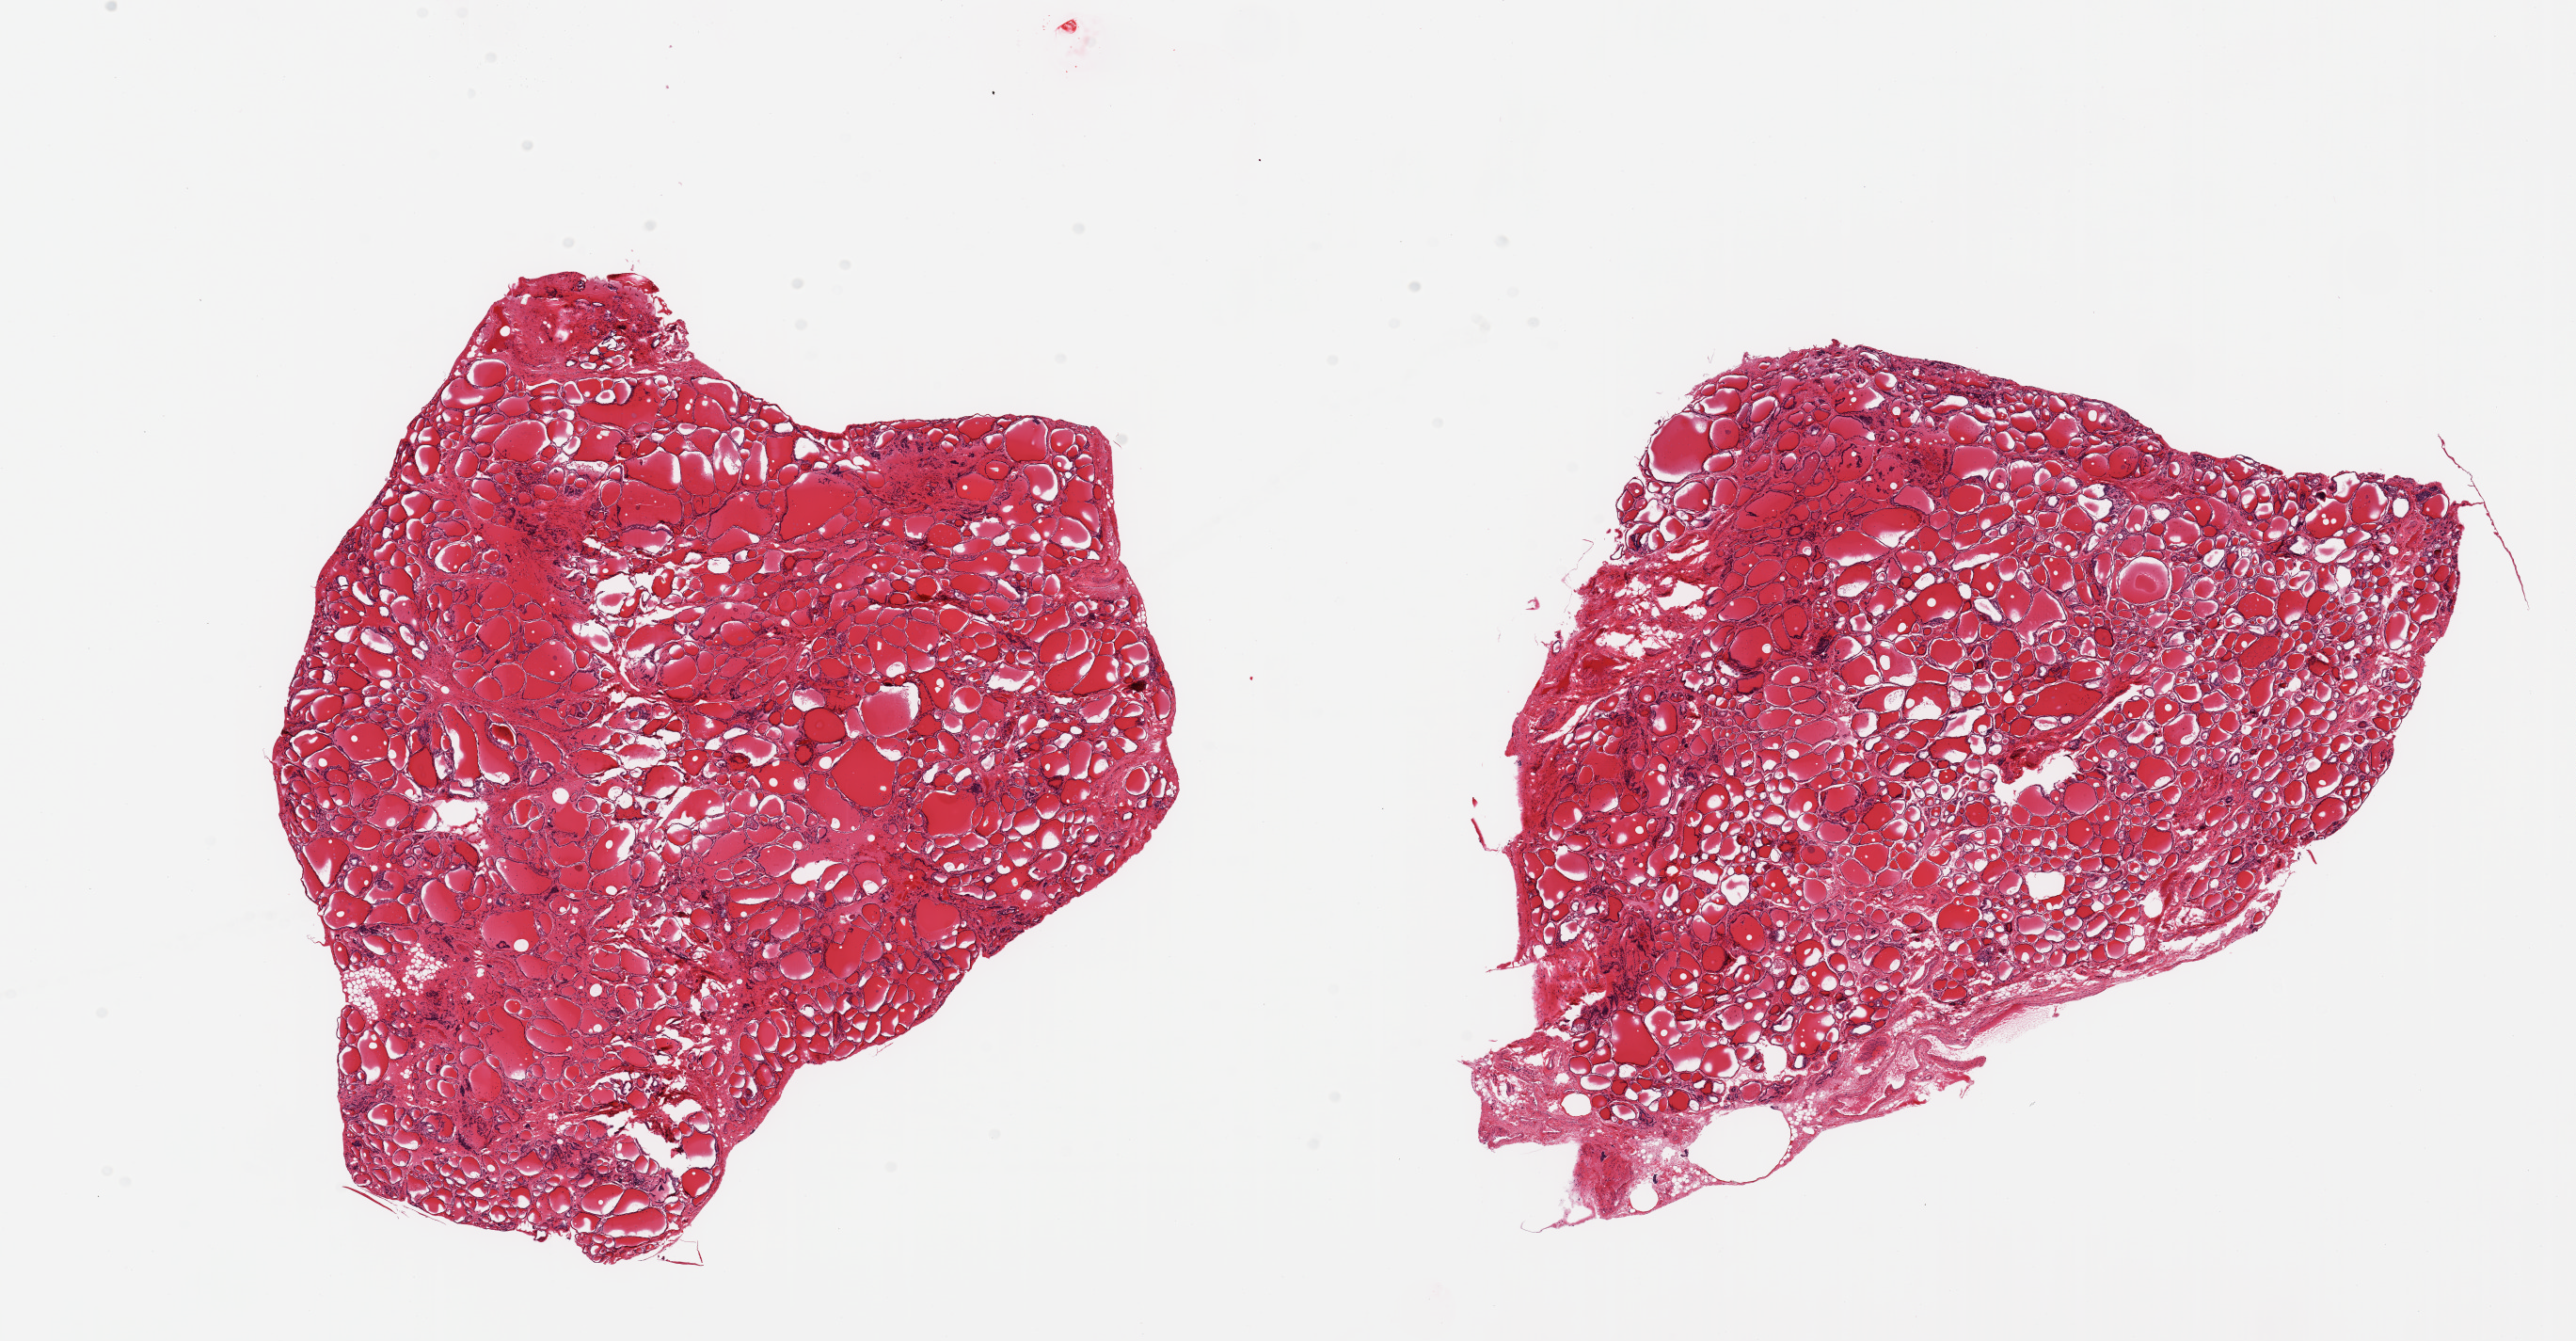
H&E whole-slide image — a low-resolution overview of the entire scanned area, about 21.7 x 11.3 mm (slide scanned at 20x); PAXgene-fixed paraffin-embedded (PFPE) section; section of thyroid (target tissue); tissue donor sample.
• reviewer comment on this tissue sample: 2 pieces; well dissected; no lesions